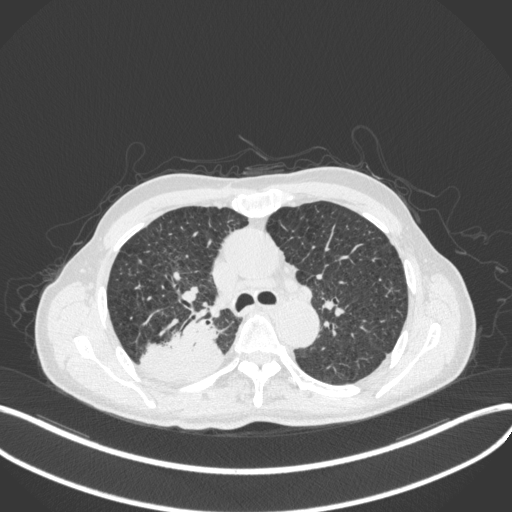
Chest CT, one axial slice. Slice 303 of 423 in the series (ordered by position). Reconstruction kernel B31f. Lung window (W 1500 / L -600 HU). 512 × 512 image matrix, field of view 400 × 400 mm. Male patient, age 79 years. From the clinical record (not read from this slice): clinical TNM (as recorded): T3 N0 M0.
Outlined on this slice (bounding box drawn by a radiologist):
- lung tumour (recorded histology: adenocarcinoma): bounding box <140,310,225,388> (left, top, right, bottom; pixels)